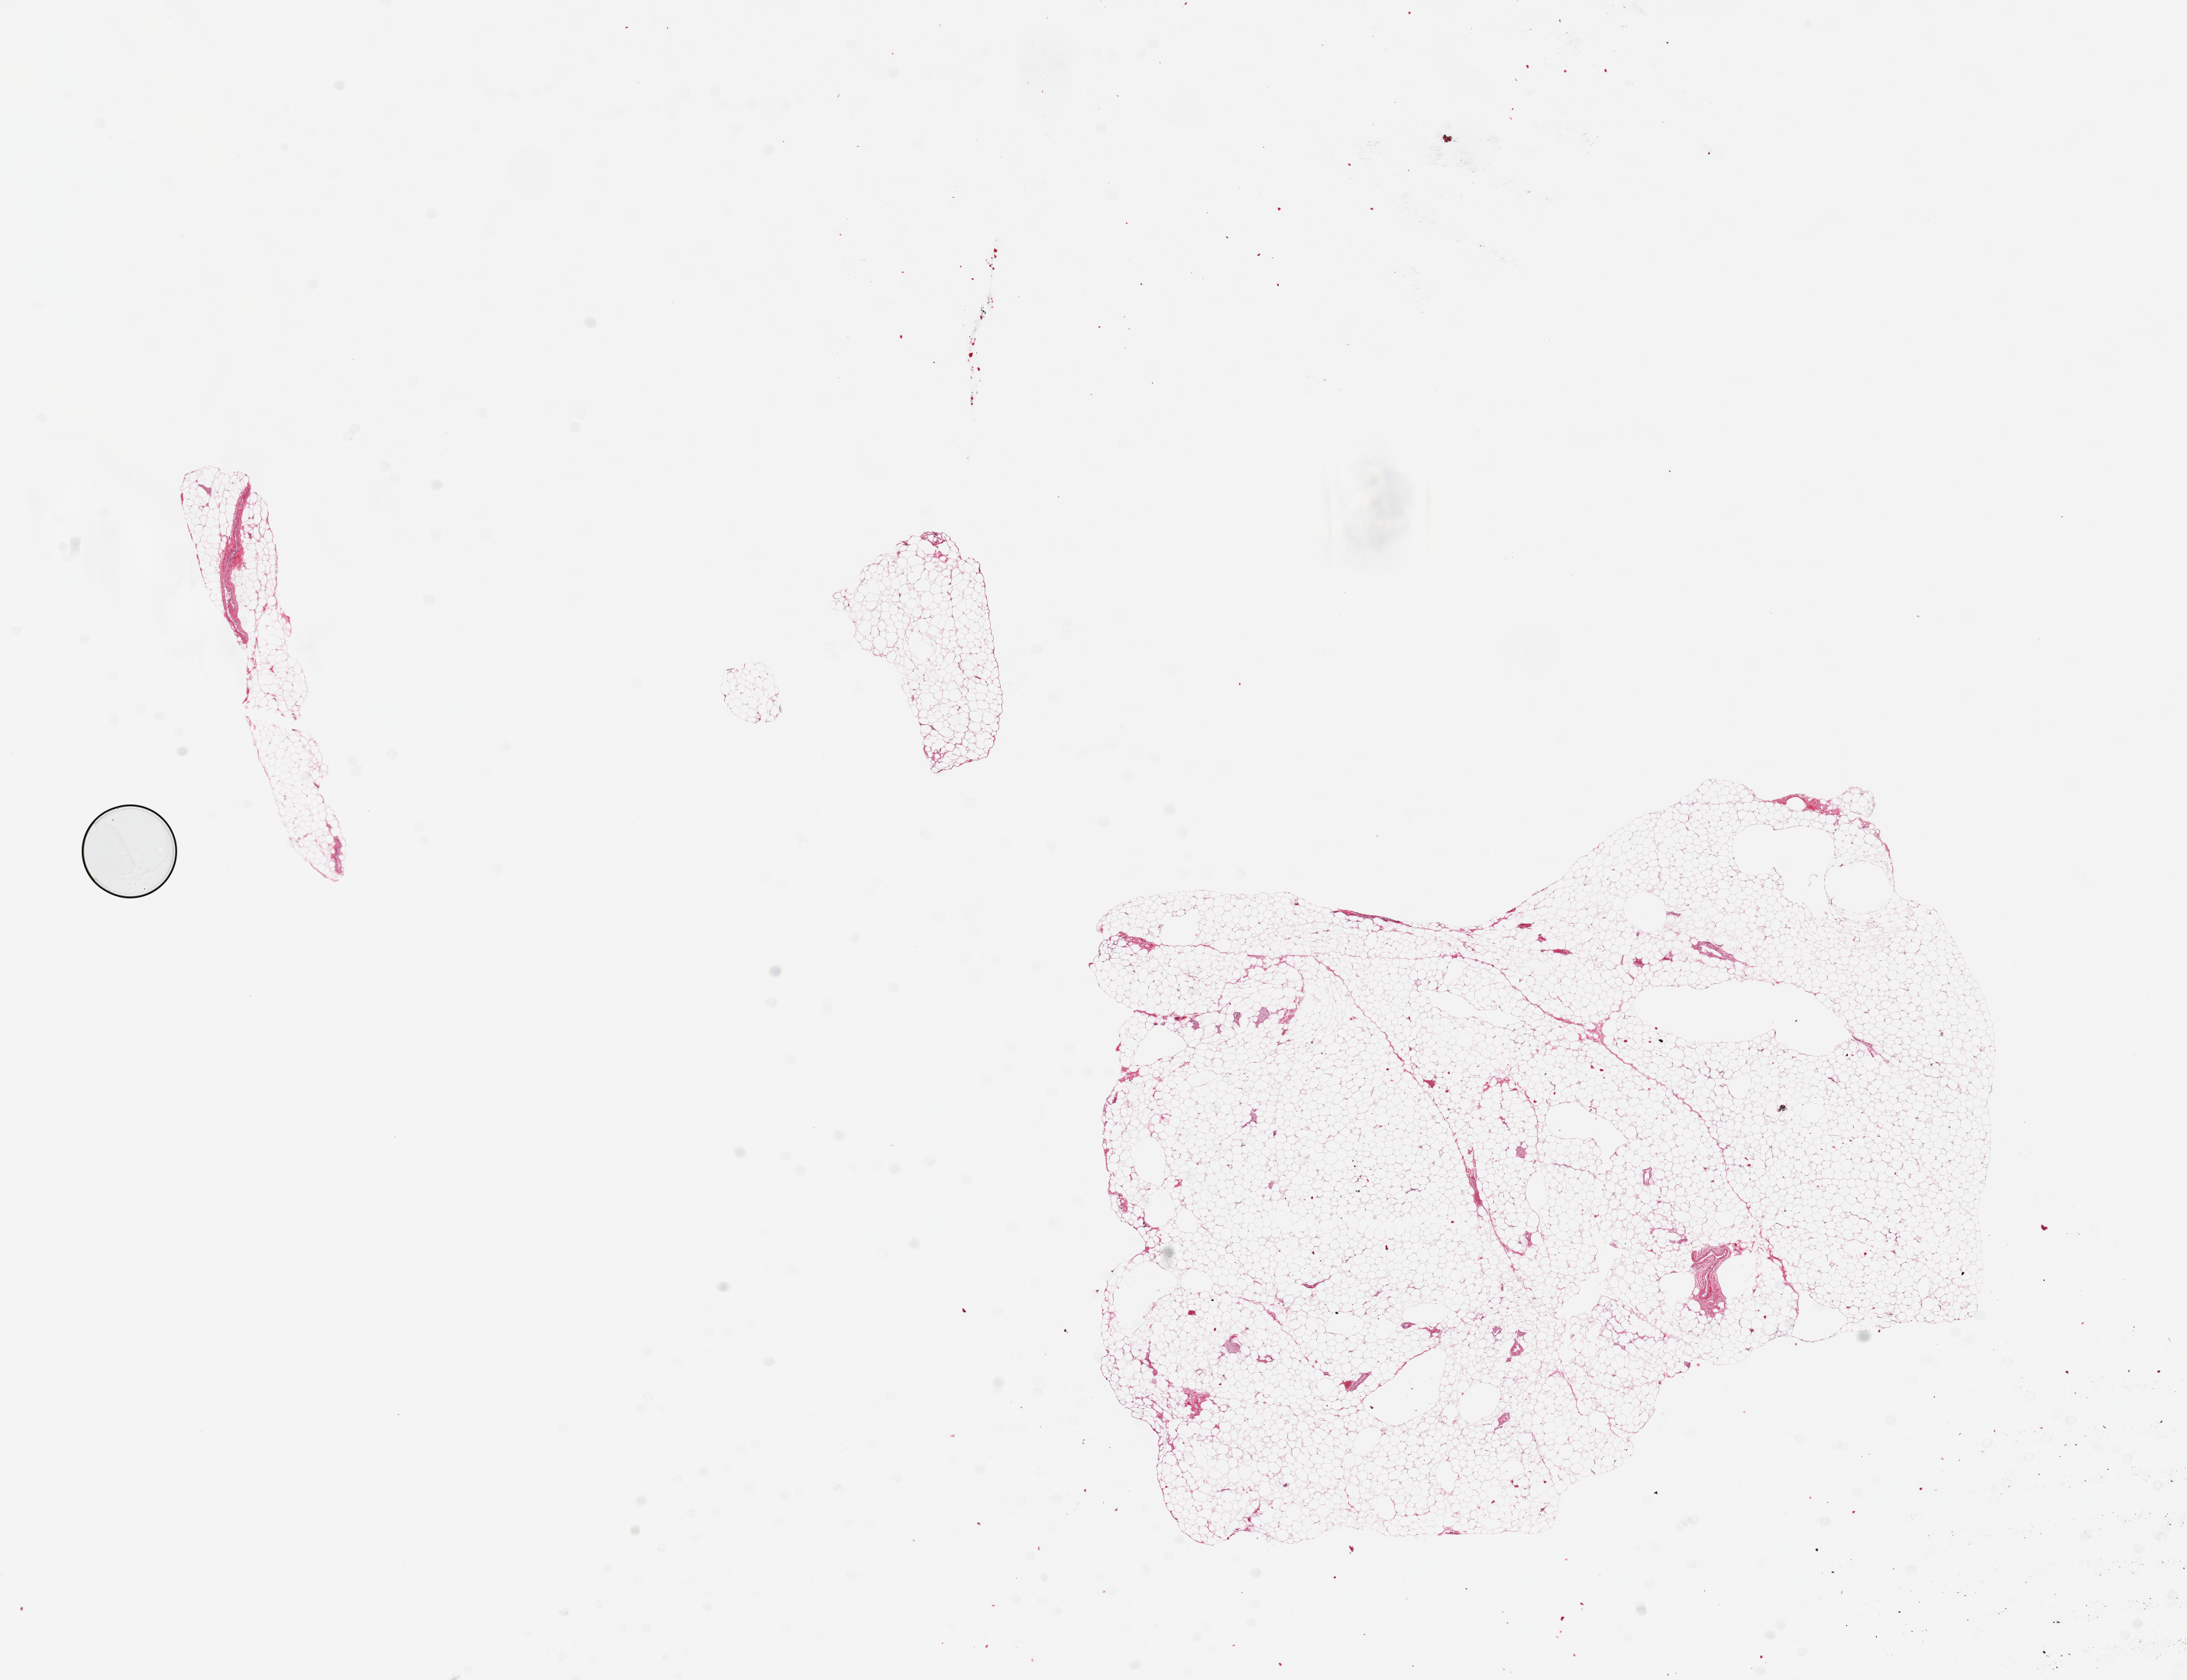
H&E whole-slide image, low-resolution overview of the scanned area, about 22.6 x 17.4 mm (from a 20x scan). PAXgene-fixed, paraffin-embedded tissue. Sampled site (target tissue): omentum. Donor tissue sample.
Review note (as recorded): 3 pieces, up to 9x7mm; no significant artifacts.